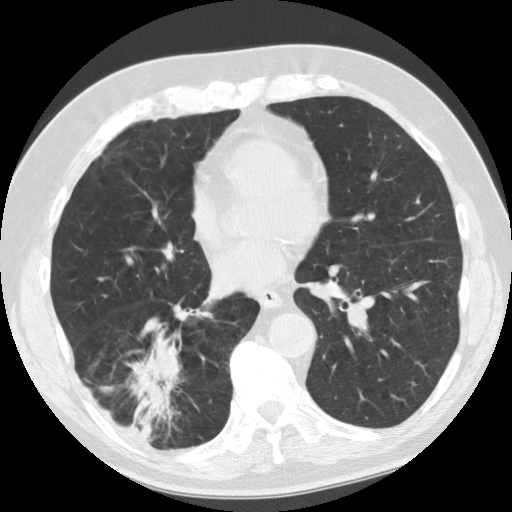
Low-dose screening chest CT, axial slice. Baseline screening round. Lung window (W 1500 / L -600 HU). Slice 84 of 135 in the series. 512 × 512 image matrix. Male, age 69 years at enrolment. Former smoker at enrolment.
Expert reader's lesion annotation, bounding box <112,332,198,441> (left, top, right, bottom; pixels). The screening reader recorded 2 non-calcified nodules or masses ≥4 mm on this exam (right lower lobe, right lower lobe); which of them this box marks is not recorded.